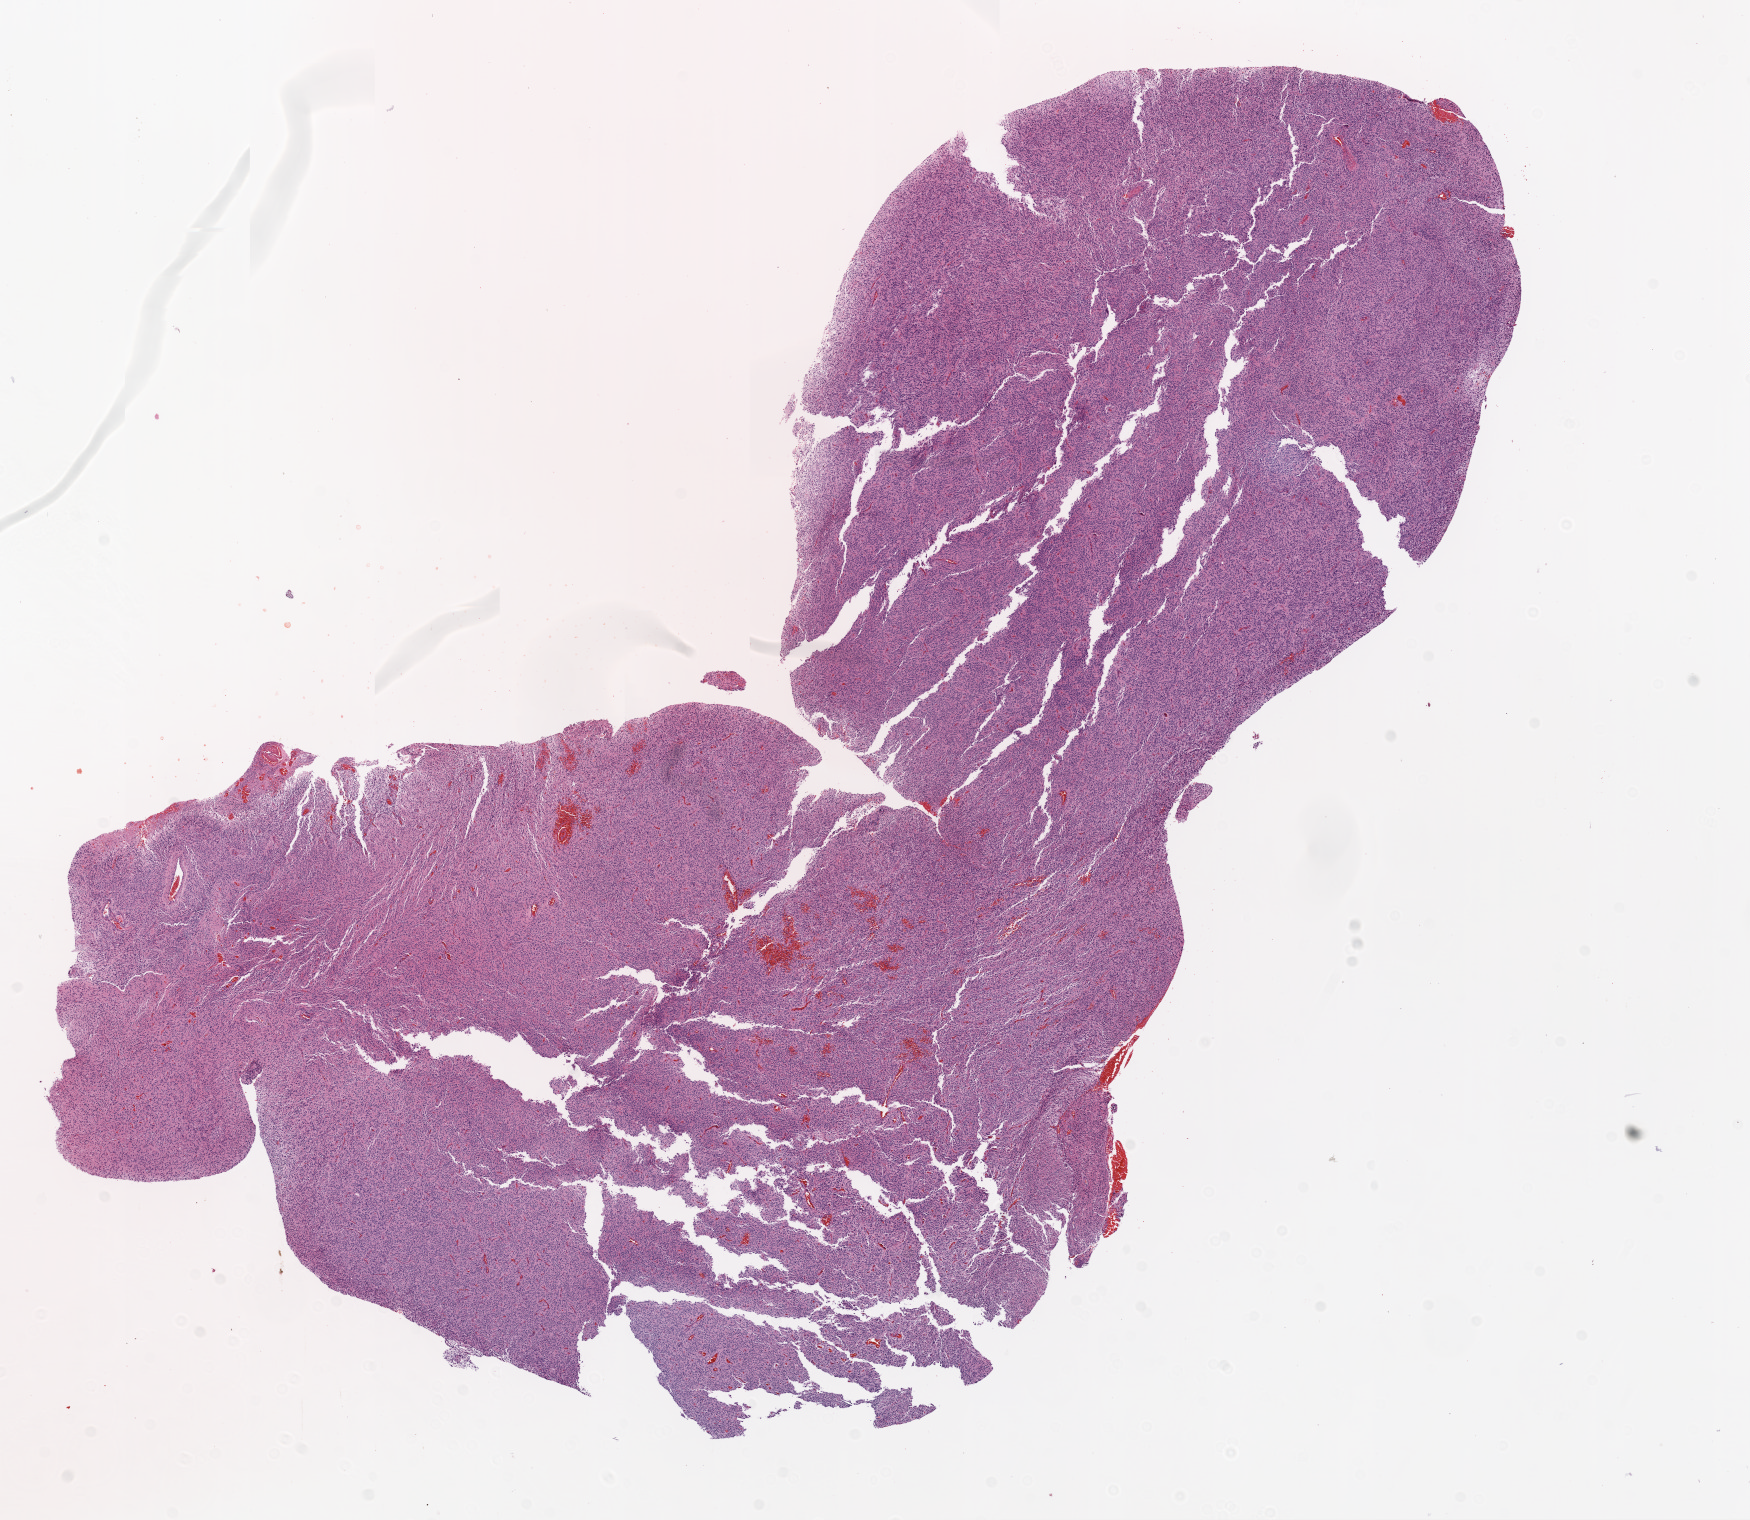
Whole-slide histology image, H&E-stained, low-resolution overview of the scanned area, about 14.0 x 12.2 mm; FFPE section; sample: primary tumour, brain. Male, age 53 years at initial diagnosis.
* diagnosis: Glioblastoma